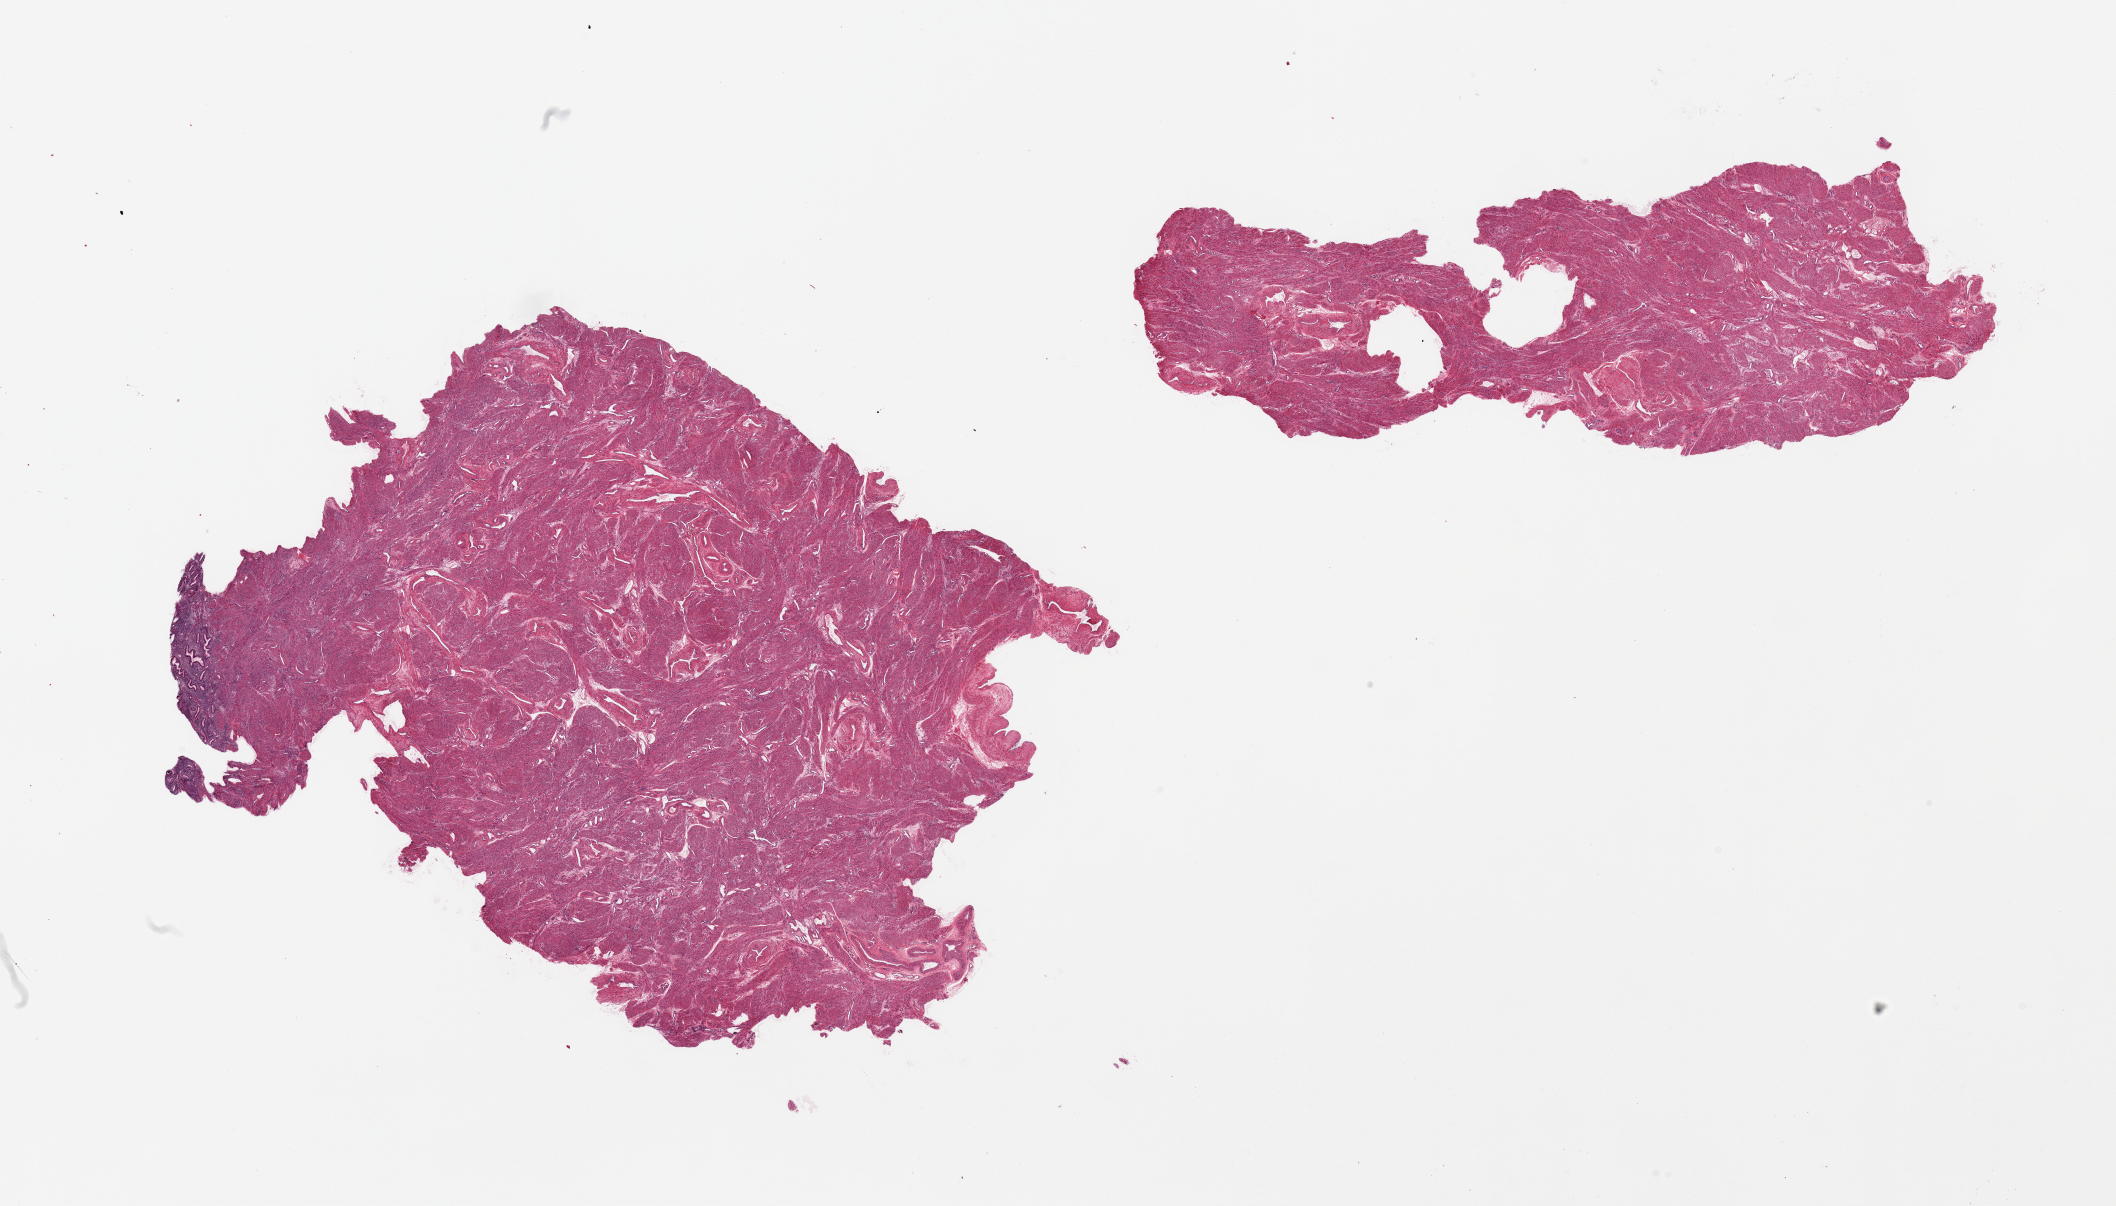
Digitized hematoxylin and eosin (H&E)-stained section, brightfield, a low-resolution overview of the entire scanned area, about 33.5 x 19.1 mm (slide scanned at 20x); PAXgene-fixed, paraffin-embedded tissue; target tissue: uterus; tissue donor sample. Donor sex: female.
Reviewer comment on this tissue sample: 2 pieces, mainly myometrium; focal endometrial glandular/stromal elements.